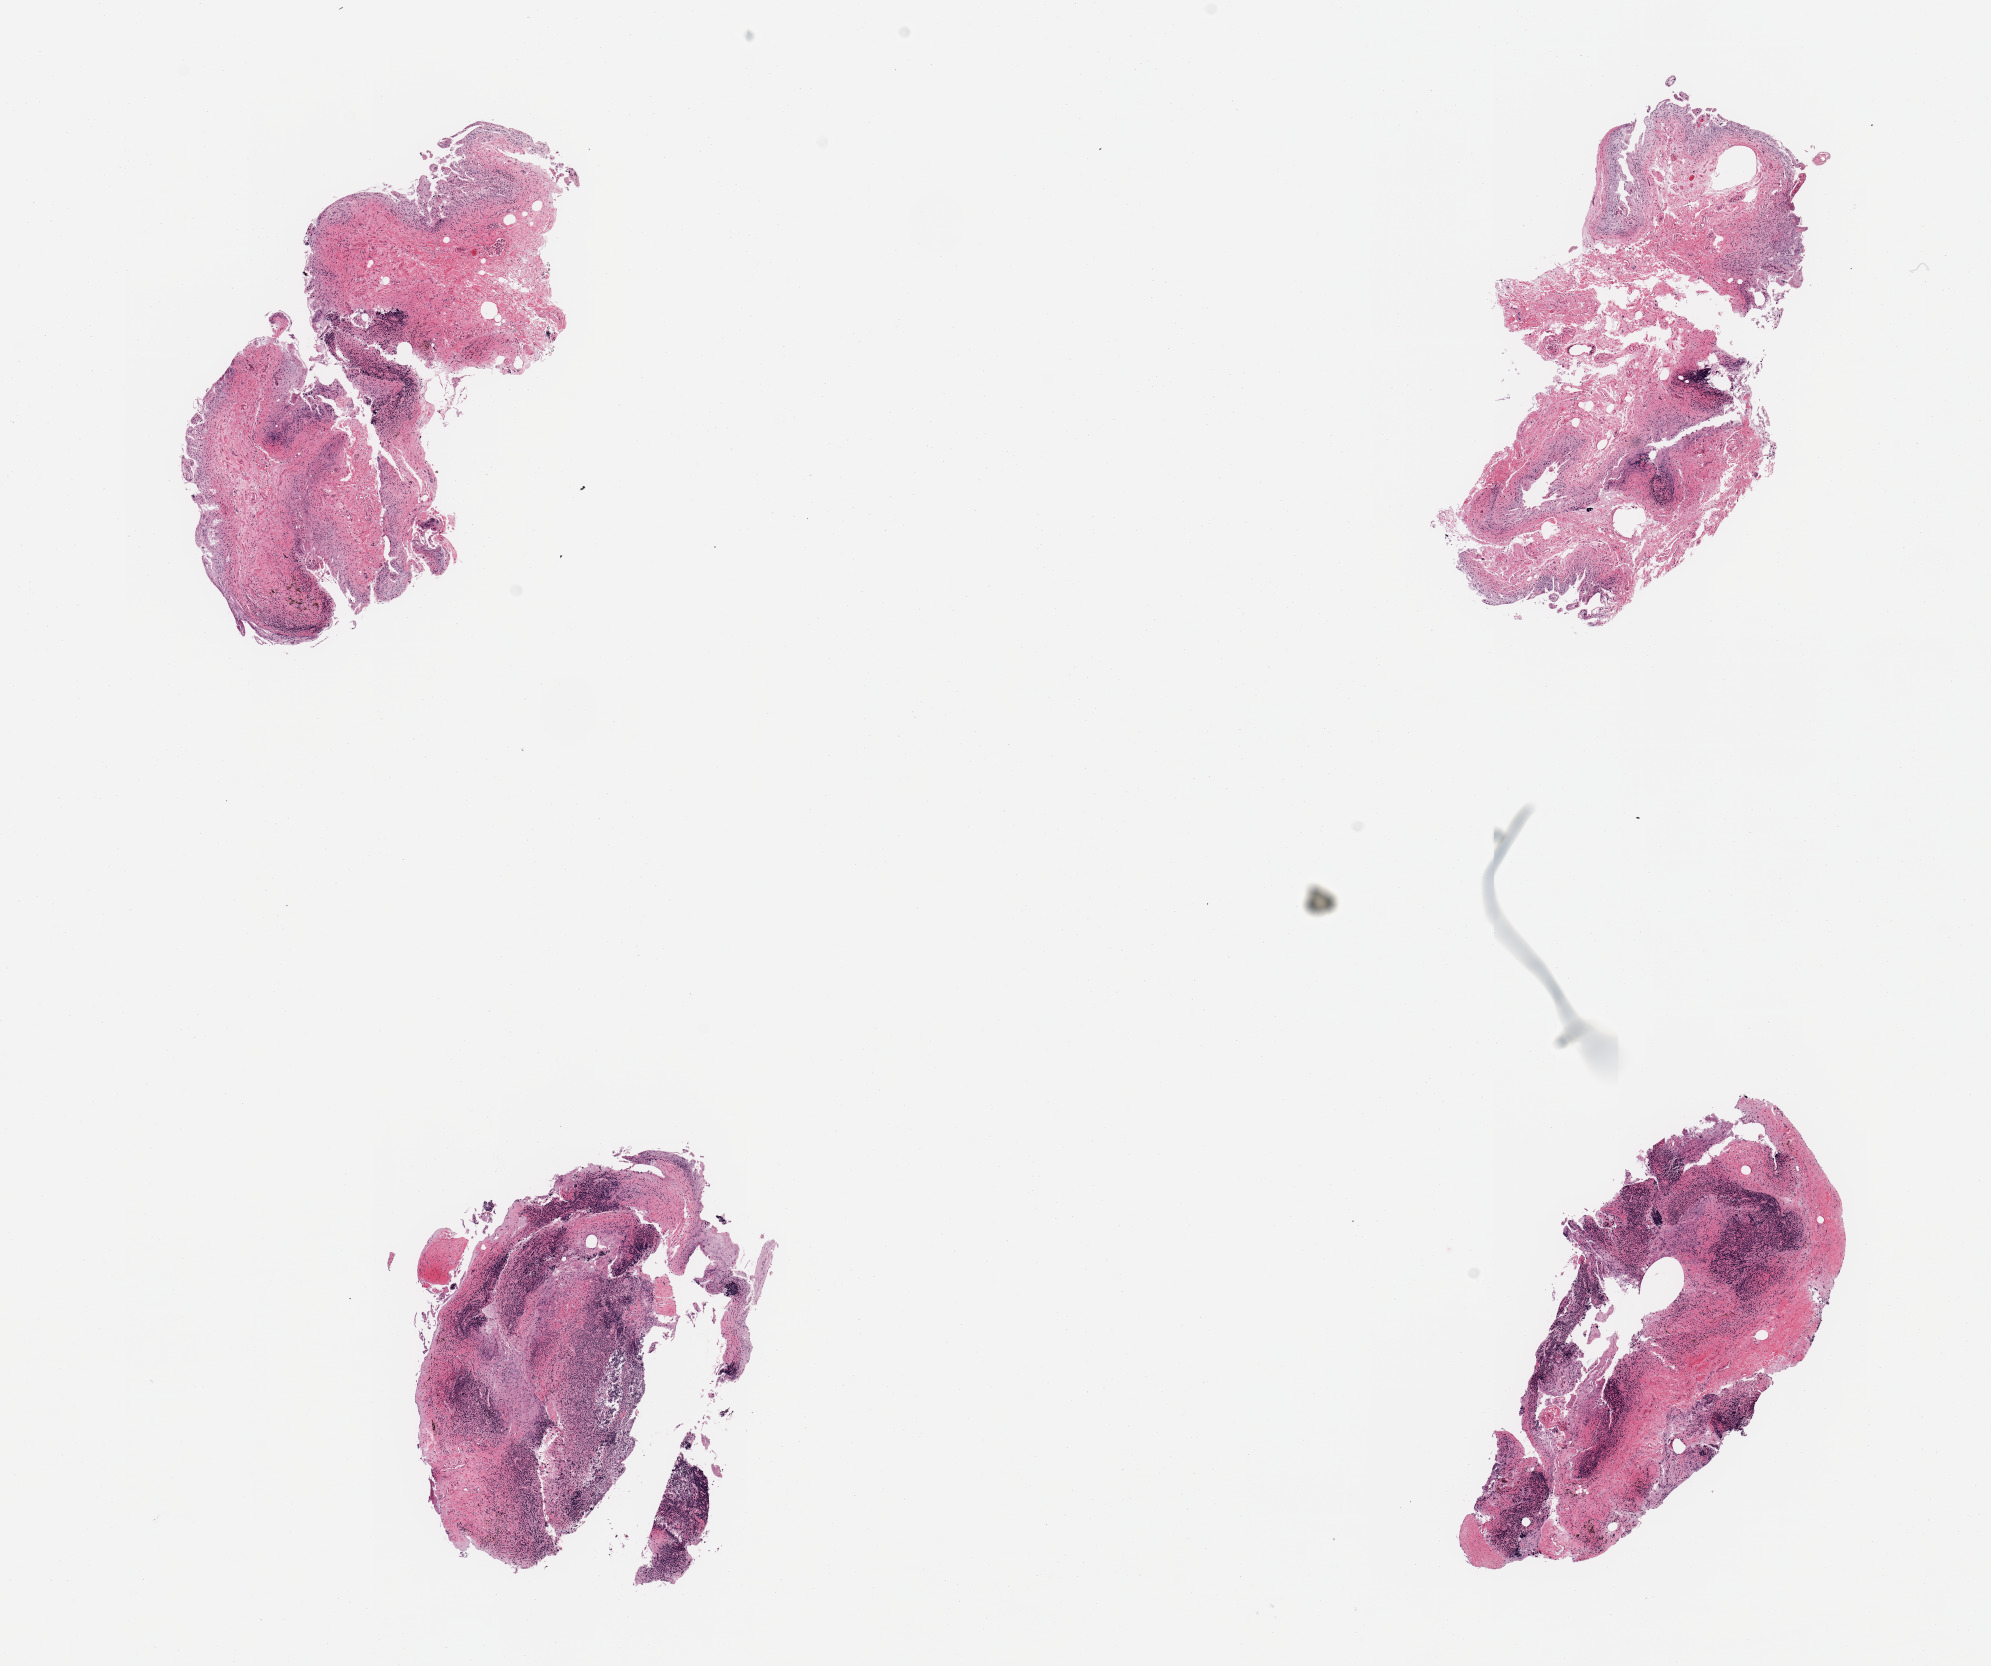
Whole-slide image, H&E stain — shown as a low-resolution overview of the whole scanned area (about 15.8 x 13.2 mm). PAXgene-fixed paraffin-embedded (PFPE) section. Sampled site (target tissue): ileum. Donor tissue sample. Male donor.
Reviewer comment on this tissue sample: 4 pieces, advanced mucosal autolysis; residual target lymphoid aggregates are ~20% of residual tissue.